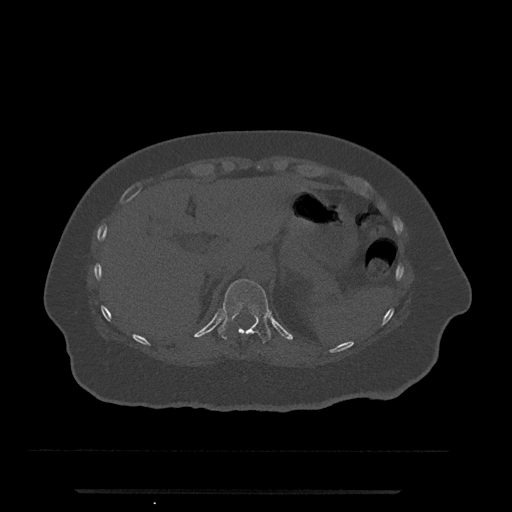
CT including the spine, one axial slice. Slice 234 of 797 in the series (ordered by position). Bone window (W 1800 / L 400 HU). 0.5 mm slice thickness. 512 × 512 image matrix. Patient: female, 51 years. From the clinical record (not read from this slice): primary cancer: neuro; vertebrae with lytic lesions (as recorded): T8.
Outlined on this slice (semi-automatically segmented with operator editing):
- T11 vertebra: bounding box <218,279,271,344> (left, top, right, bottom; pixels)